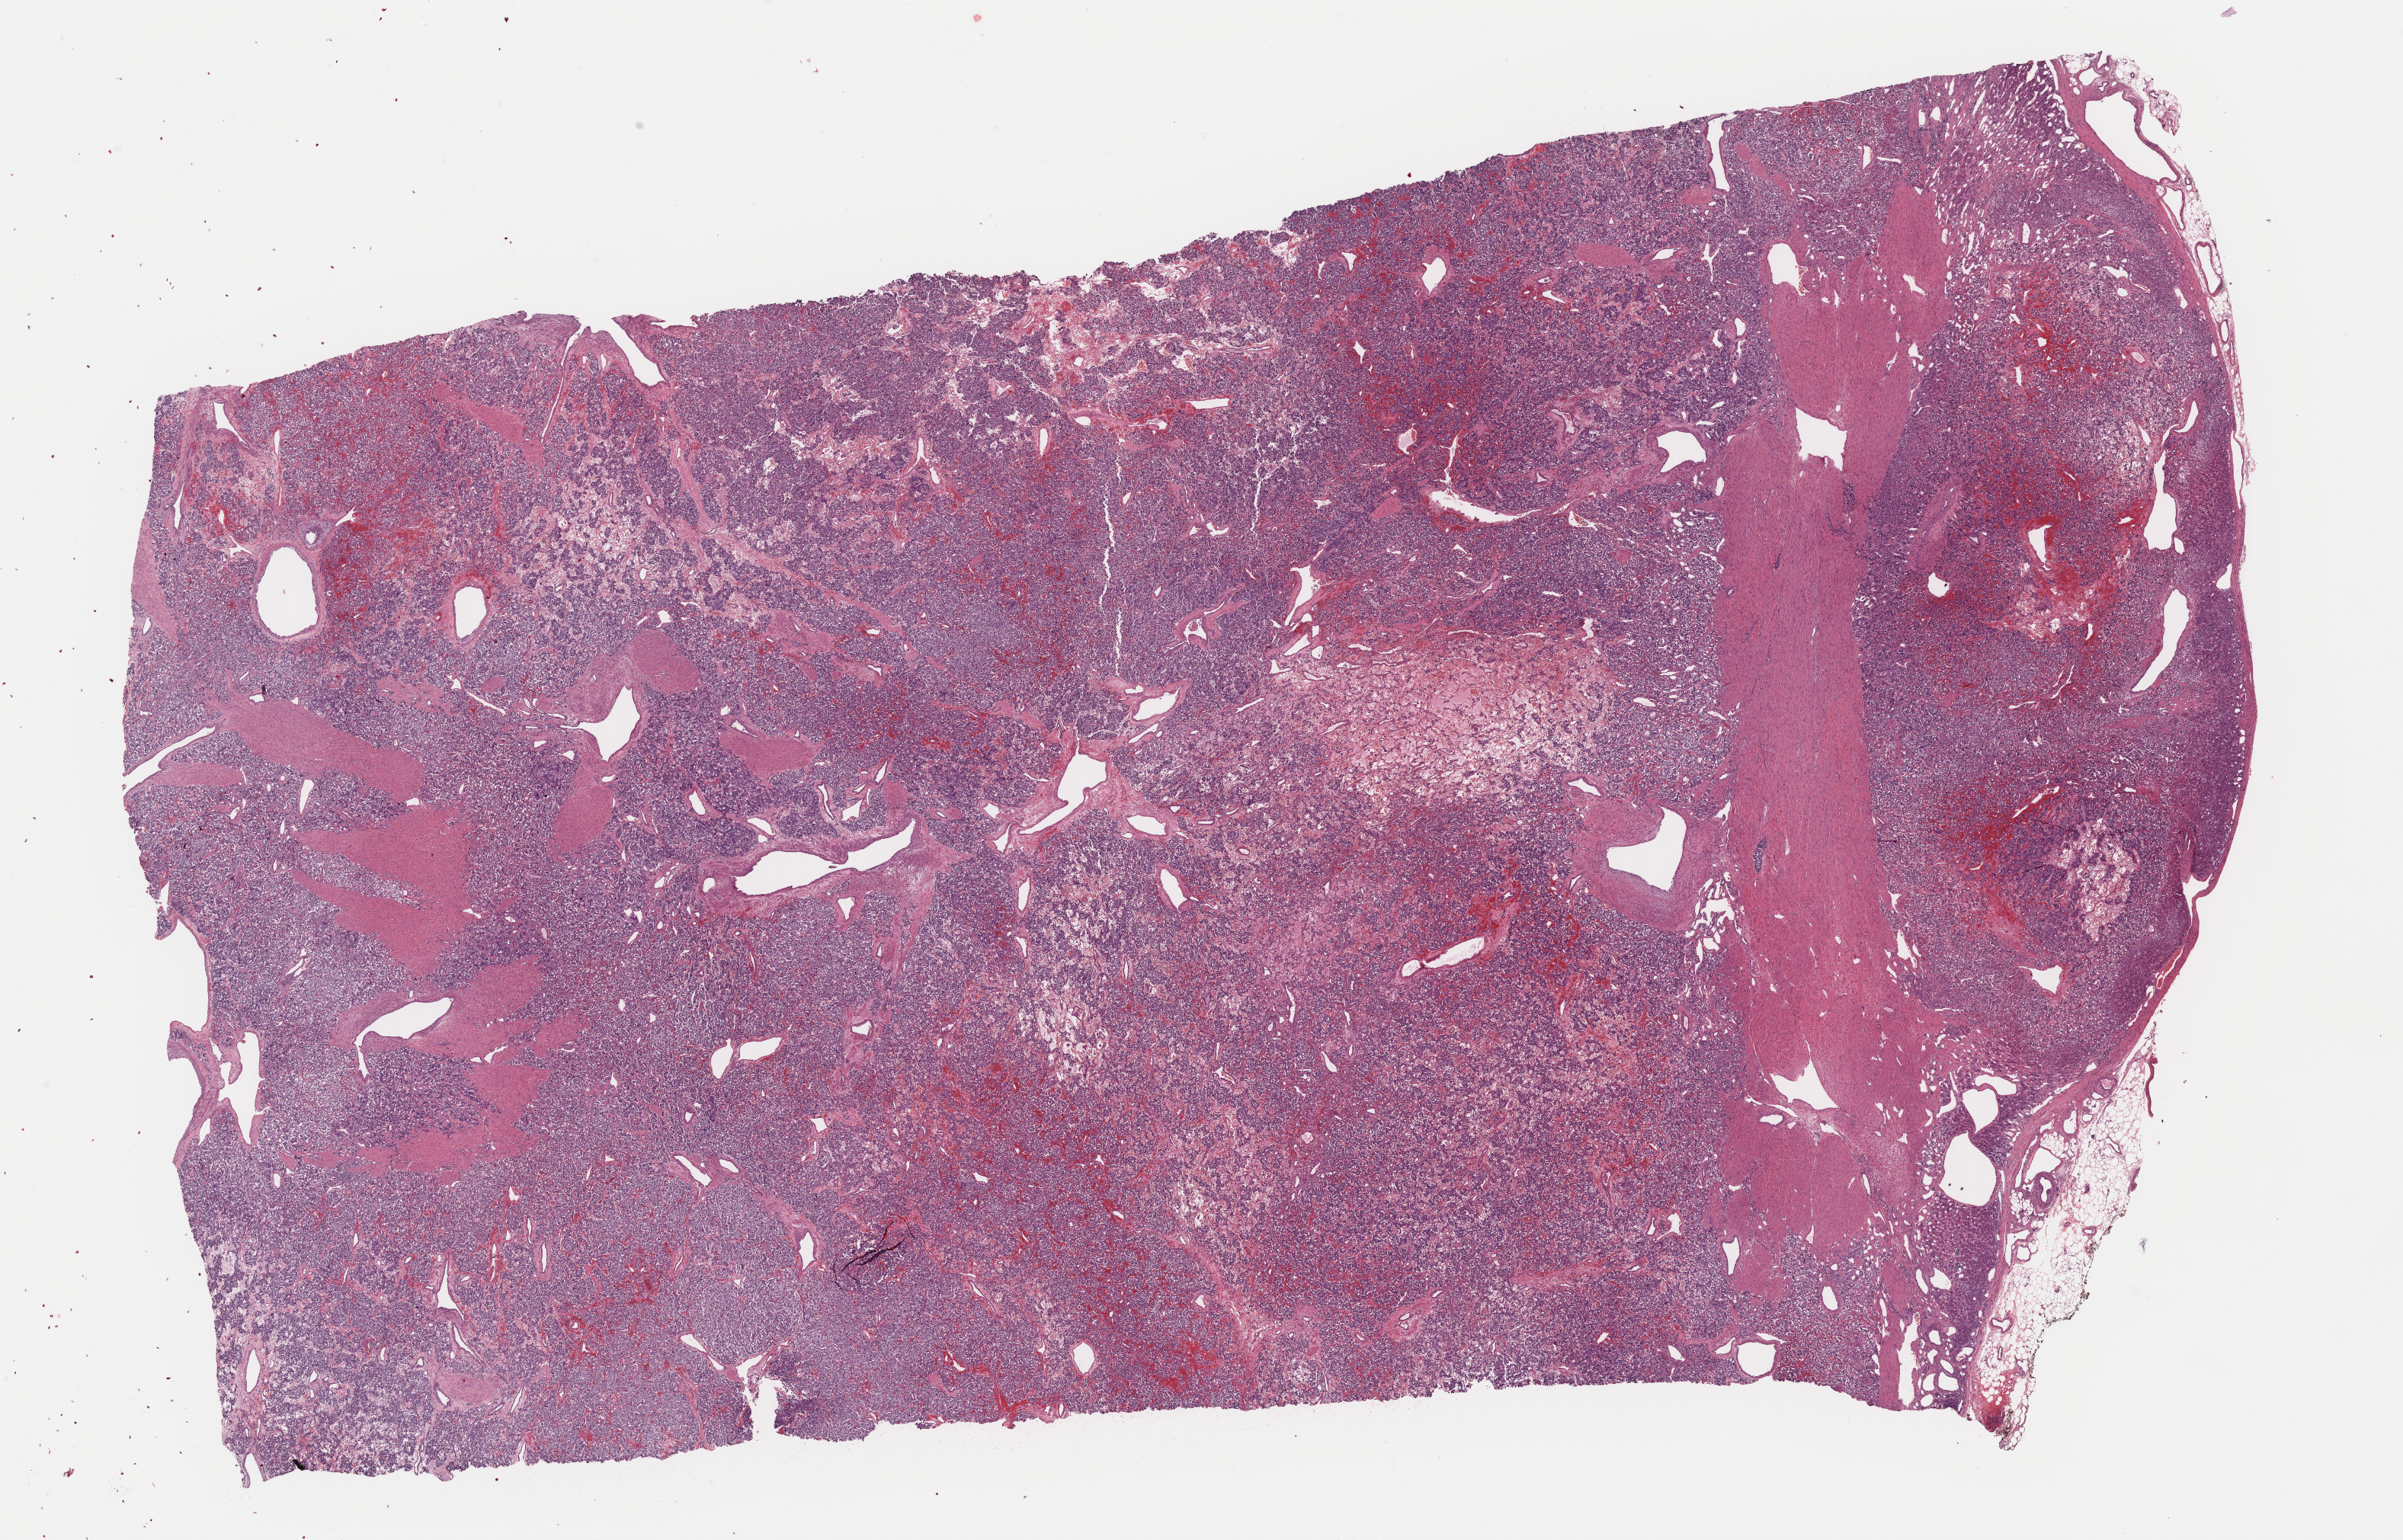
Hematoxylin and eosin (H&E) stained whole-slide image, whole scanned area (about 24.9 x 15.9 mm, acquisition: 40x scan) shown as a low-resolution overview; formalin-fixed paraffin-embedded (FFPE) diagnostic section; sample: primary tumour, adrenal gland. Patient: male, age at initial diagnosis 48 years.
* diagnosis: Pheochromocytoma, NOS (medulla of adrenal gland)